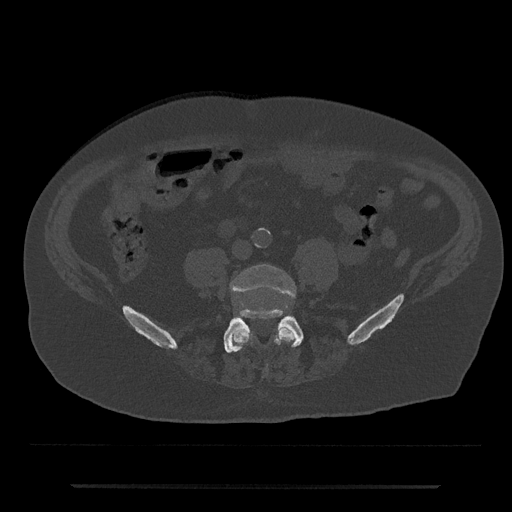
CT including the spine, one axial slice; position 315 of 797 along the scan axis; bone window (W 1800 / L 400 HU); 512 × 512 image matrix, field of view 434 × 434 mm. Patient: male, 80 years. From the clinical record (not read from this slice): primary cancer: prostate; vertebrae with lytic lesions (as recorded): L1, T11.
Outlined on this slice (semi-automatically segmented with operator editing):
- L4 vertebra: bounding box [x1, y1, x2, y2] px = [230, 264, 296, 349]
- L5 vertebra: [223, 309, 304, 353]